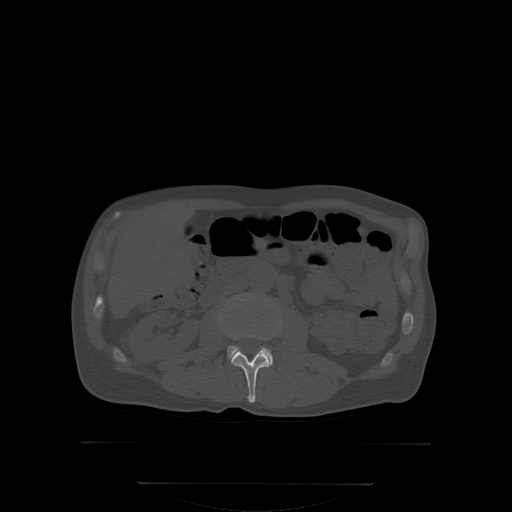
CT including the spine, one axial slice. Position 132 of 350 along the scan axis. Bone window (W 1800 / L 400 HU). 2.5 mm slice thickness. 512 × 512 image matrix. Patient: male, 58 years. From the clinical record (not read from this slice): primary cancer: prostate; vertebrae with lytic lesions (as recorded): L1.
Outlined on this slice (semi-automatically segmented with operator editing):
- L2 vertebra: bounding box (x1, y1, x2, y2) in pixels: (232, 334, 269, 402)
- L3 vertebra: (227, 346, 272, 366)